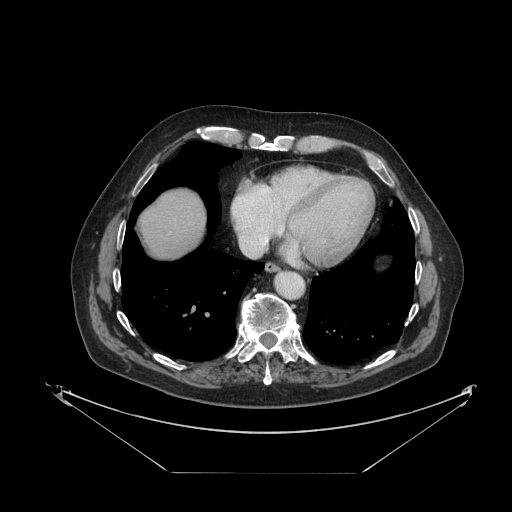
Contrast-enhanced abdominal CT, one axial slice; slice 118 of 121 in the series (ordered by position); intravenous contrast given; soft-tissue window (W 400 / L 40 HU); 2.5 mm slice thickness; 512 × 512 image matrix, field of view 500 × 500 mm. Male patient, age 68 years. From the clinical record (not read from this slice): diagnosis: colorectal cancer liver metastases, imaged before liver resection.
Structures marked on this image (manually delineated by an expert):
- liver: bounding box [x1, y1, x2, y2] px = [140, 190, 206, 258]
- planned liver remnant (the part of the liver to remain after resection): [140, 190, 206, 258]